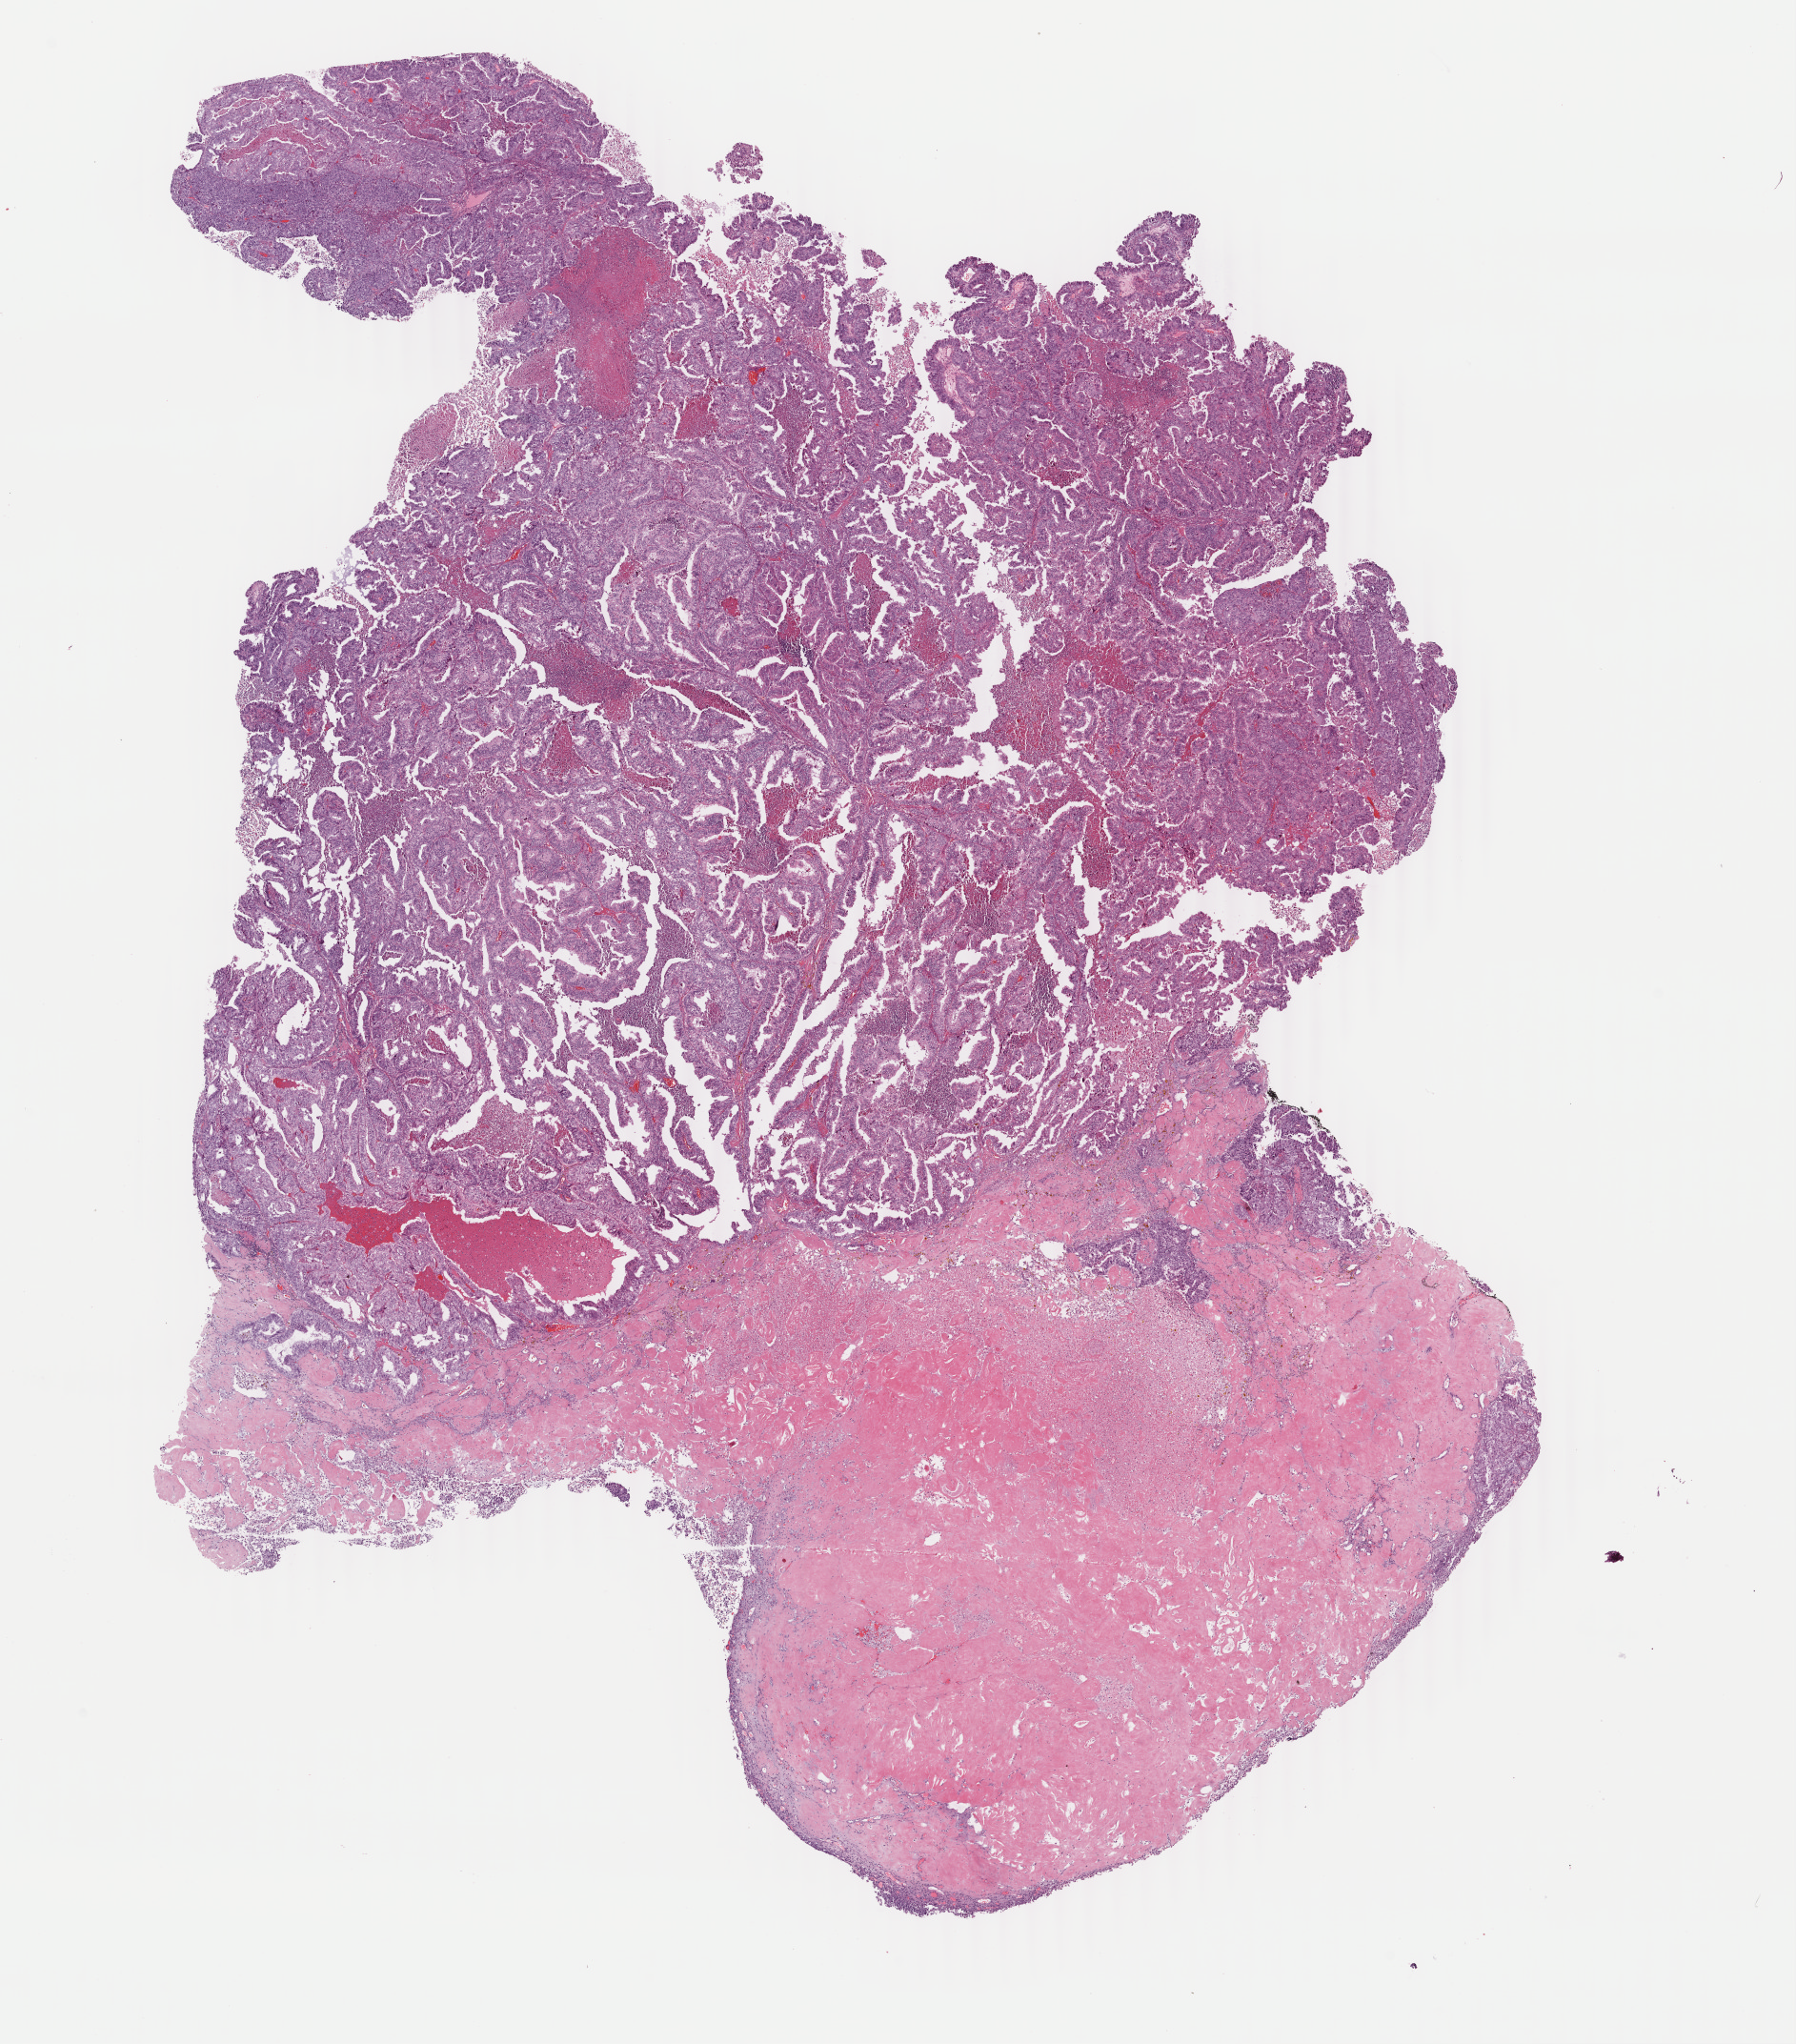
Whole-slide histology image, Hematoxylin and eosin (H&E) stained, low-resolution overview of the scanned area, about 15.0 x 17.1 mm (slide scanned at 40x). Frozen section from the bottom of the tissue portion. Uterus, primary tumour sample. Patient: female, age at initial diagnosis 74 years.
Pathologic diagnosis: Endometrioid adenocarcinoma, NOS (endometrium).